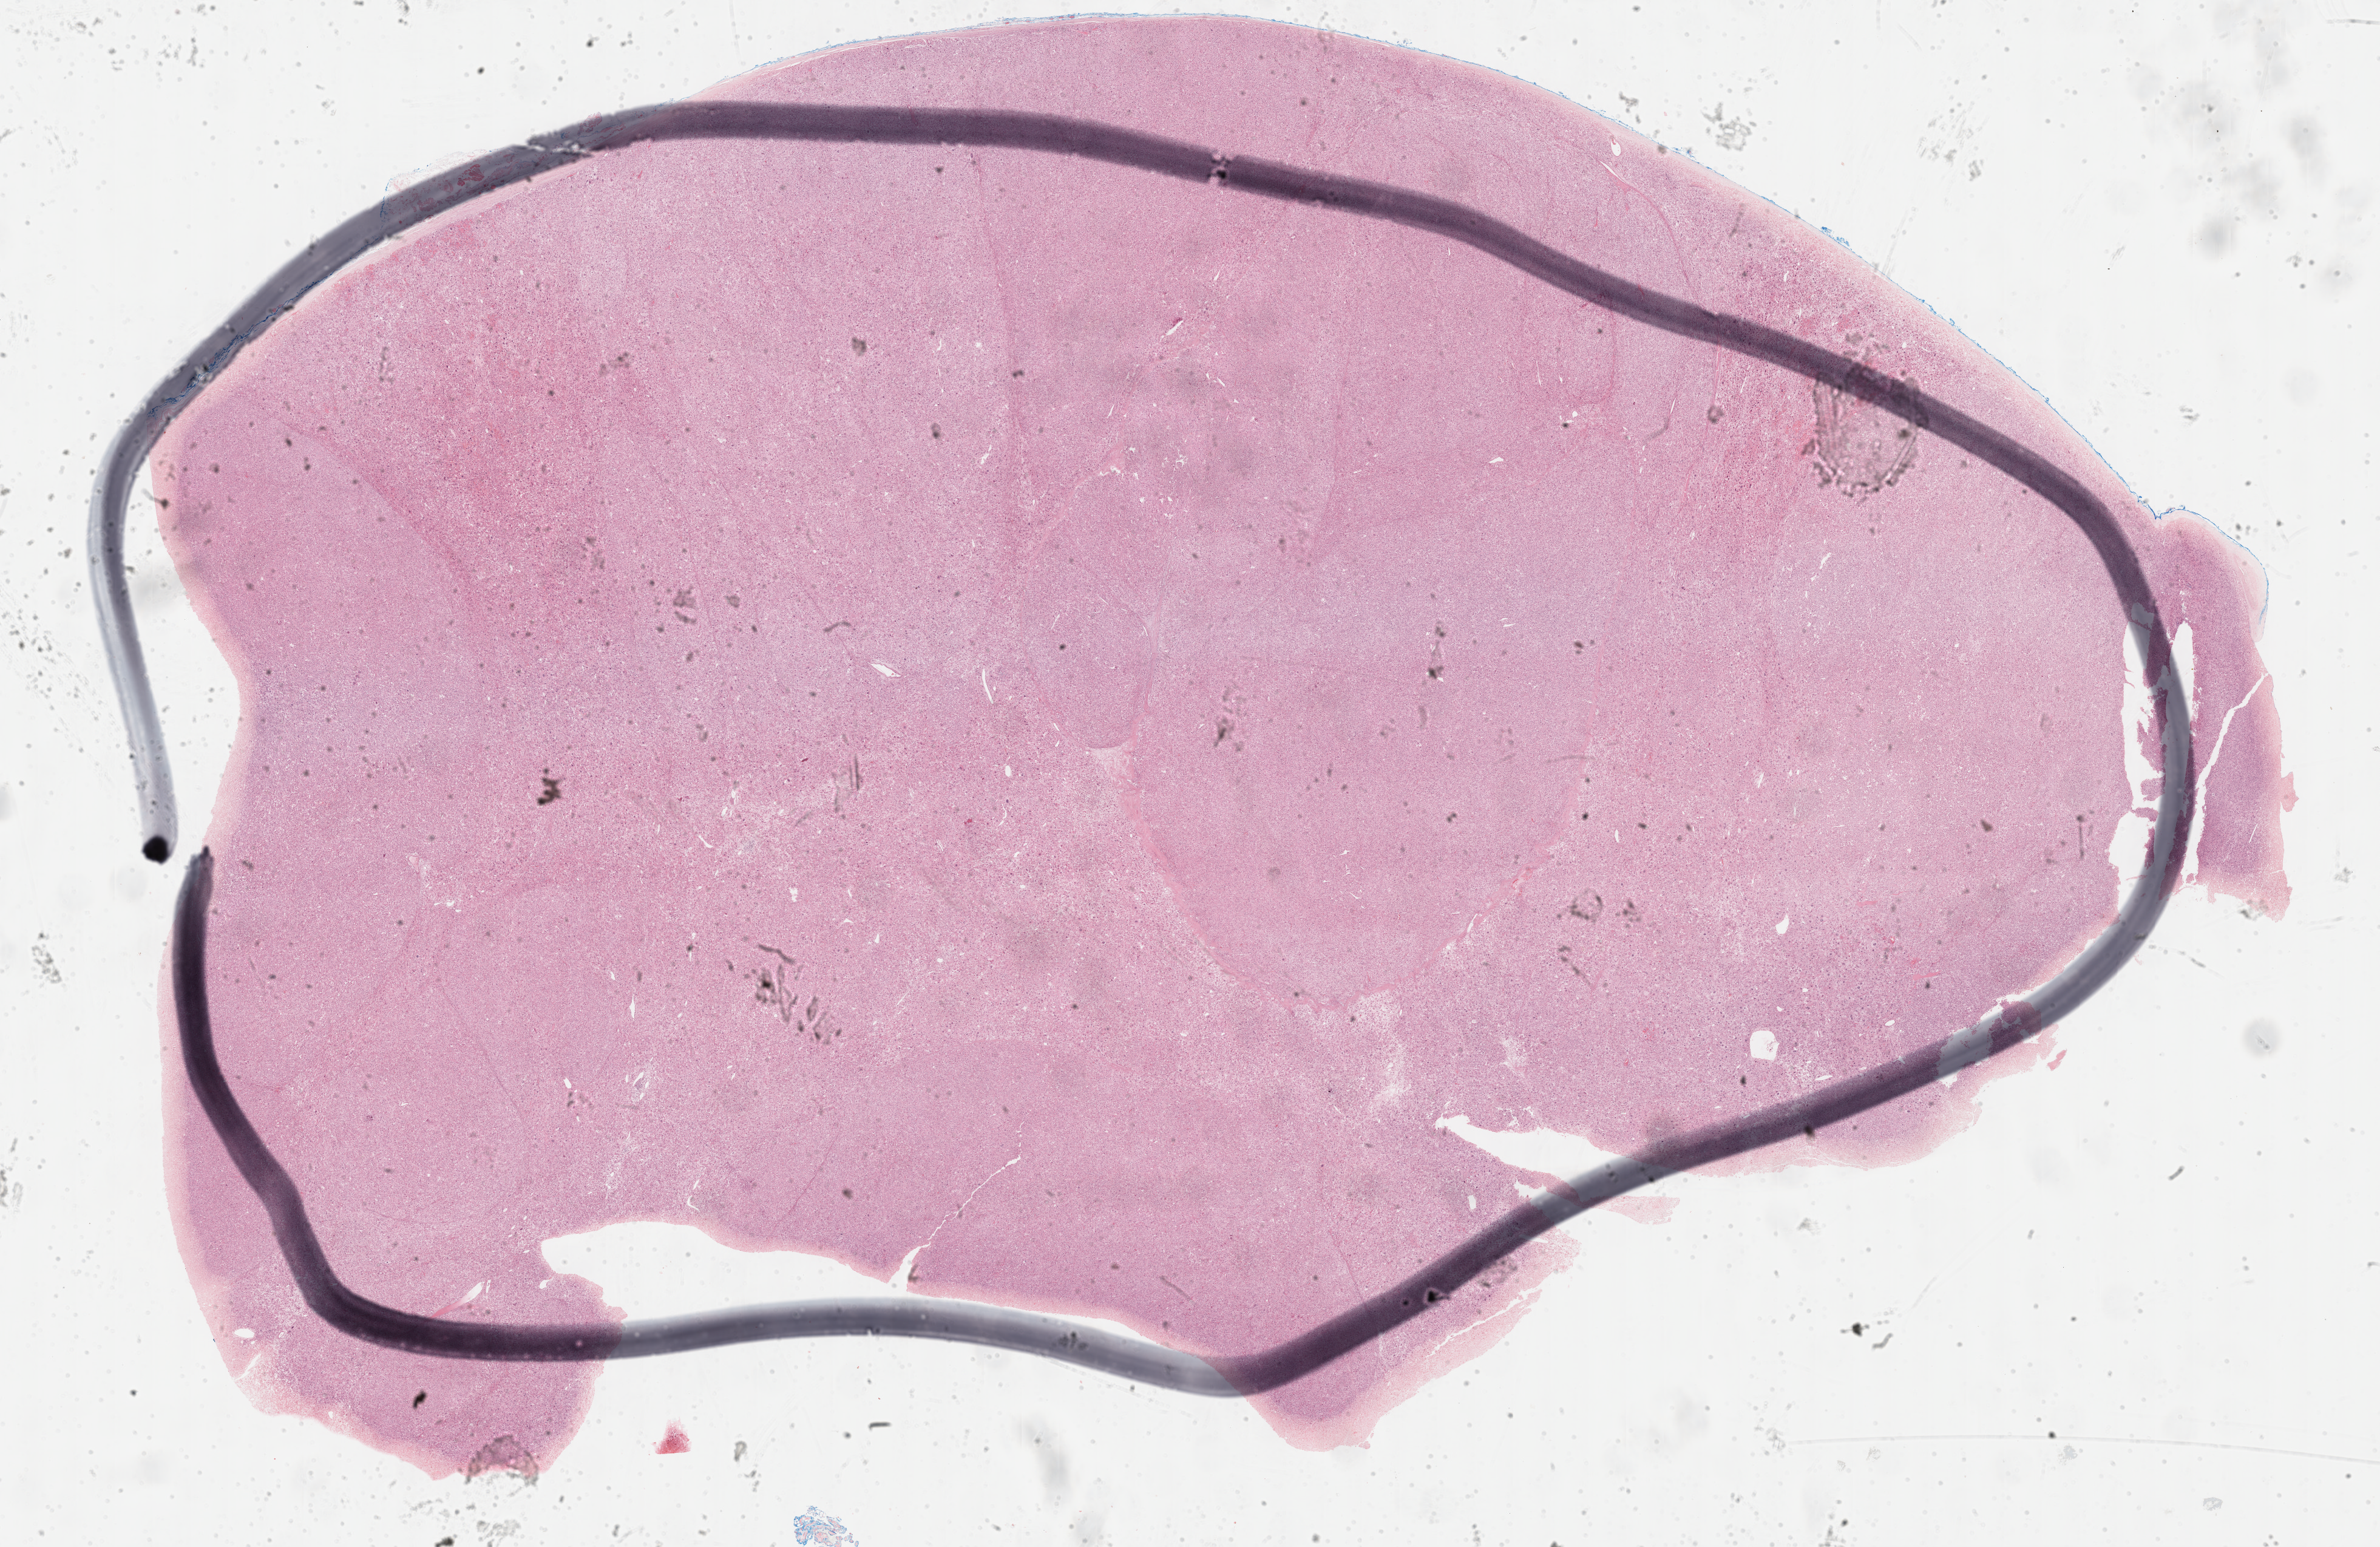
H&E-stained whole-slide image — whole scanned area (about 31.7 x 20.6 mm, acquisition: 40x scan) shown as a low-resolution overview; FFPE section; sample: primary tumour, adrenal cortex. Patient: male, age at initial diagnosis 45 years.
Histologic diagnosis: Adrenal cortical carcinoma (cortex of adrenal gland).